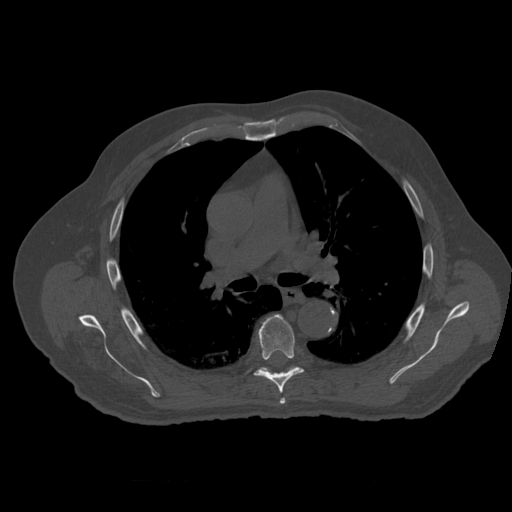
CT including the spine, one axial slice. Slice 380 of 399 in the series (ordered by position). Reconstruction kernel STANDARD. 120 kVp. Bone window (W 1800 / L 400 HU). 1.25 mm slice thickness. 512 × 512 image matrix, field of view 407 × 407 mm. Patient age 73 years. From the clinical record (not read from this slice): primary cancer: prostate.
Annotated regions visible in this slice (semi-automatic segmentation, software-assisted and operator-edited):
- T5 vertebra: bounding box <280,398,286,405> (left, top, right, bottom; pixels)
- T6 vertebra: <255,315,304,394>
- T7 vertebra: <261,367,295,373>